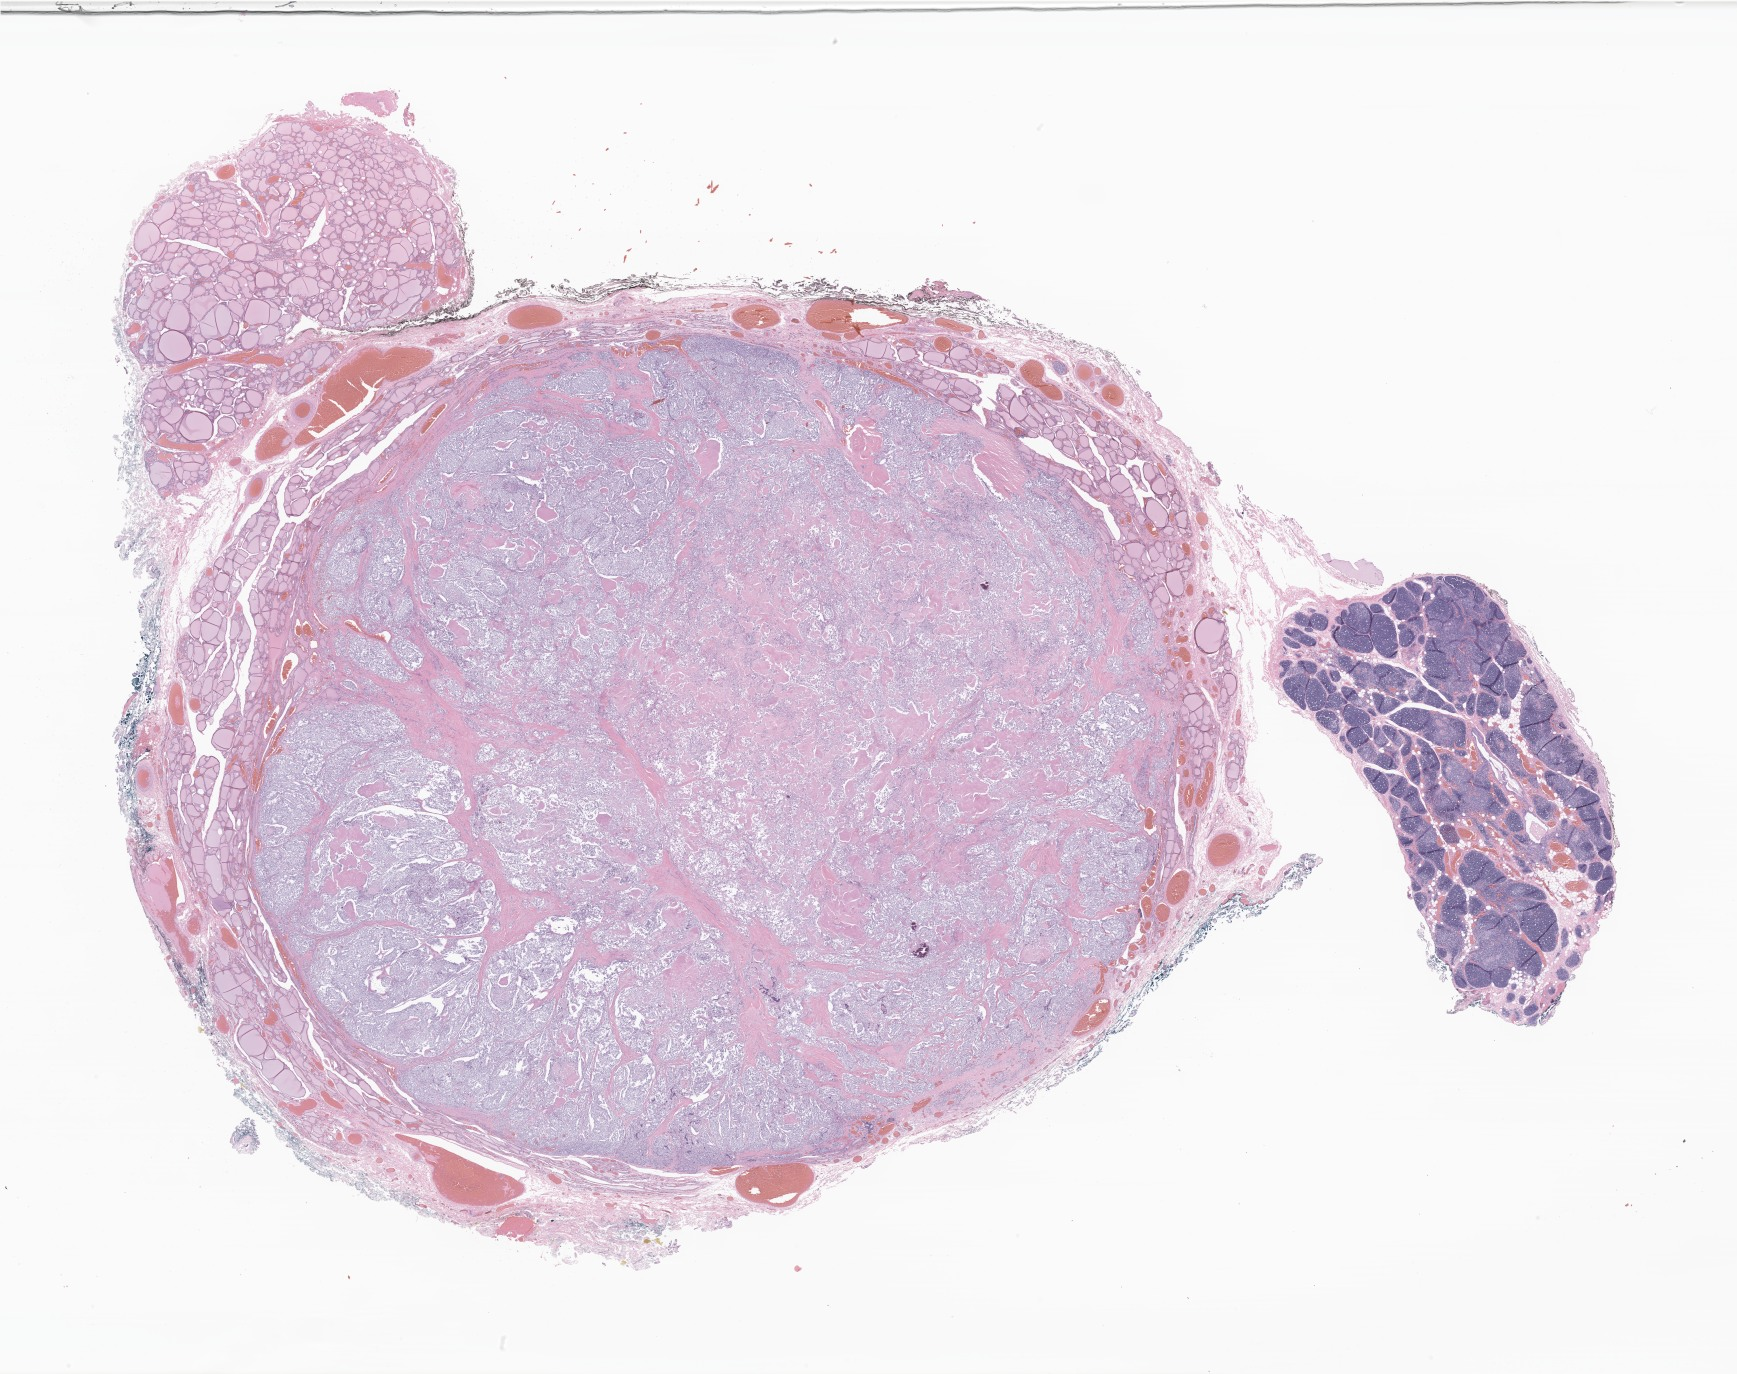
Whole-slide image, H&E stain of tumor tissue from the thyroid, shown as a low-resolution overview of the whole scanned area (about 29.3 x 23.2 mm); formalin-fixed paraffin-embedded section. Patient female; age 213 months.
Diagnosis (ICD-O-3 morphology term): Medullary carcinoma, NOS.